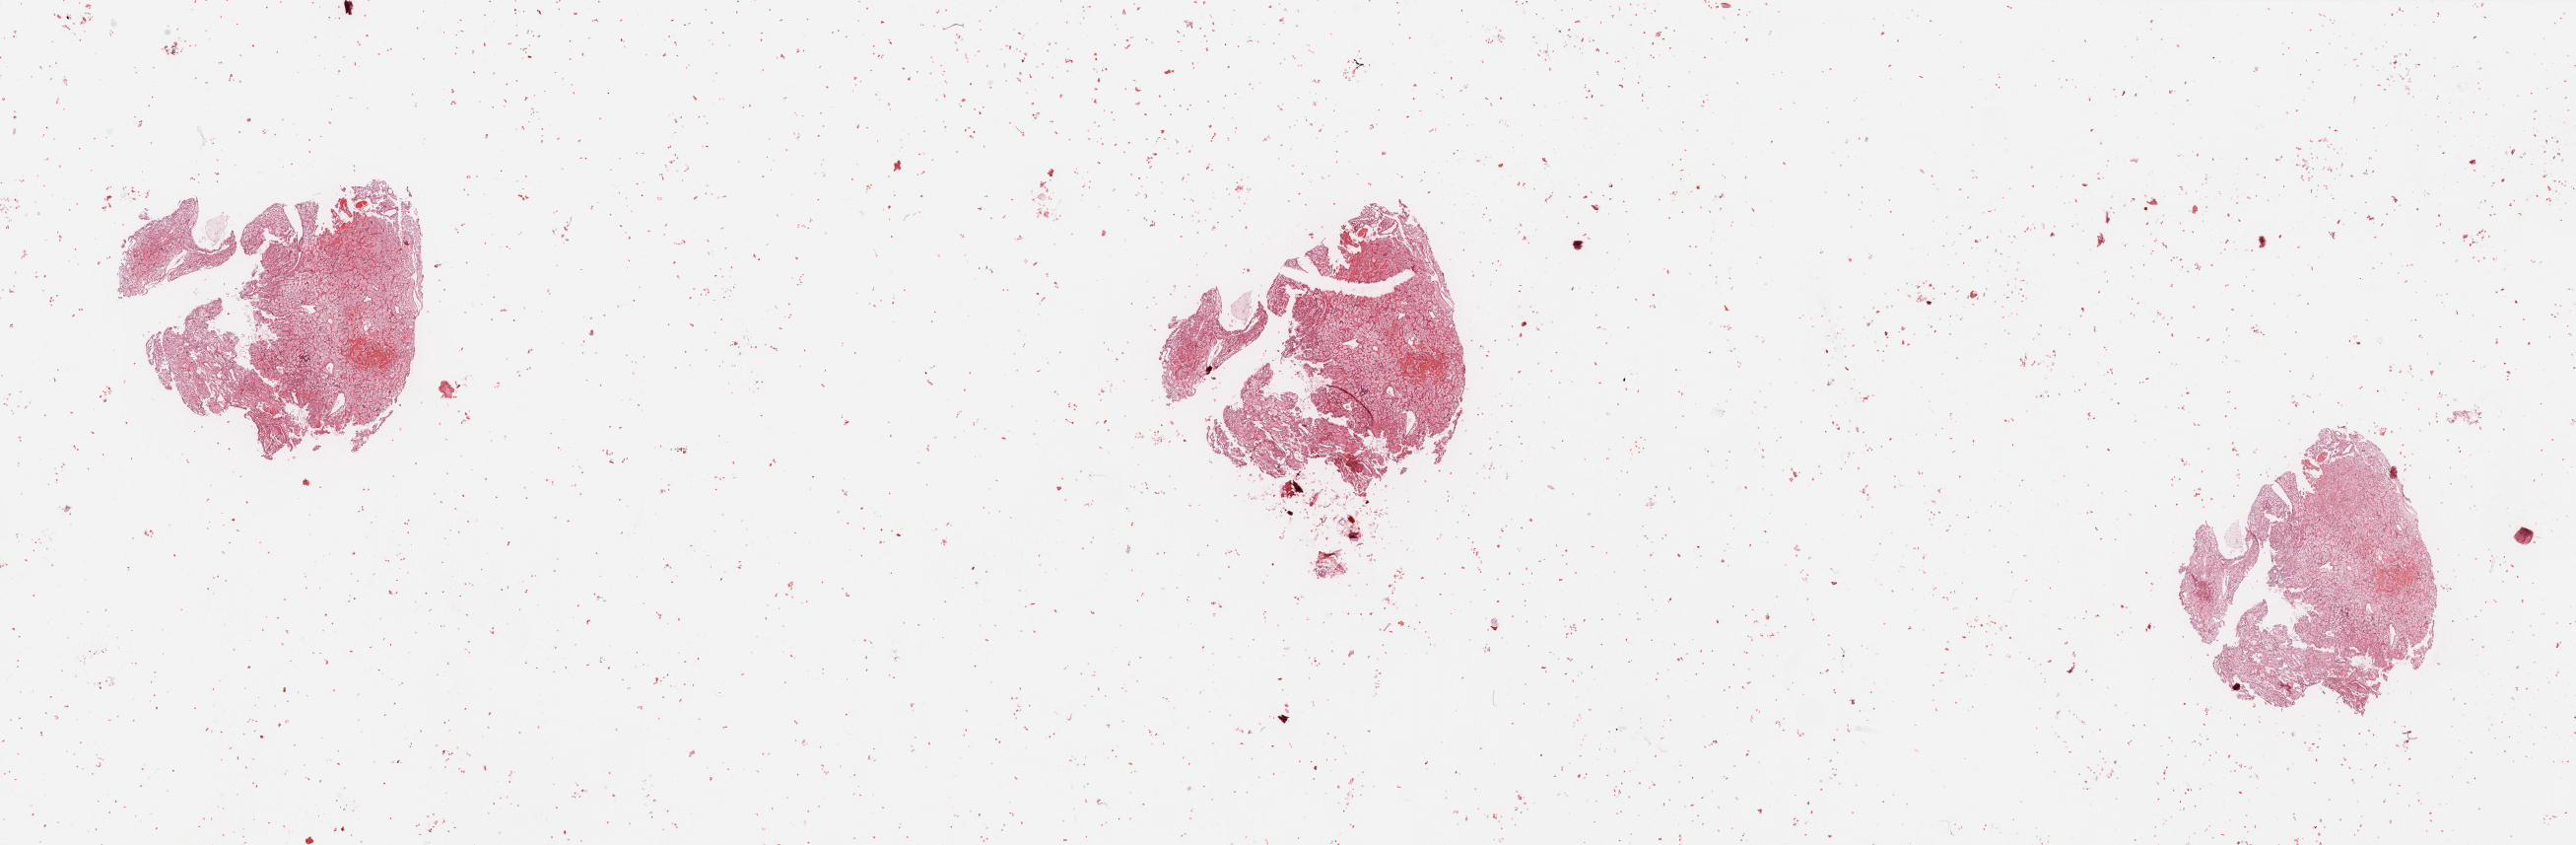
Whole-slide histology image, H&E-stained — whole scanned area (about 41.3 x 13.6 mm, acquisition: 20x scan) shown as a low-resolution overview, tumour tissue sample, sampled site: kidney. 68-year-old male patient. Slide review estimates, as recorded: tumour nuclei 85%, necrosis 5%.
Diagnosis: Renal cell carcinoma, NOS.